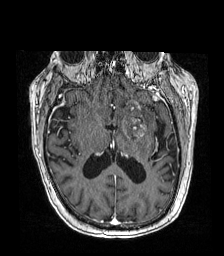
Brain MRI from a brain-tumour surgery series, one axial slice; slice 85 of 192 in the series (ordered by position); T1-weighted post-contrast; 1 mm slice thickness; 224 × 256 image matrix. From the clinical record (not read from this slice): histopathology: Metastatic carcinoma from lung primary.
Outlined on this slice (outlined manually by an expert reader):
- tumour: bounding box <117,115,148,139> (left, top, right, bottom; pixels)